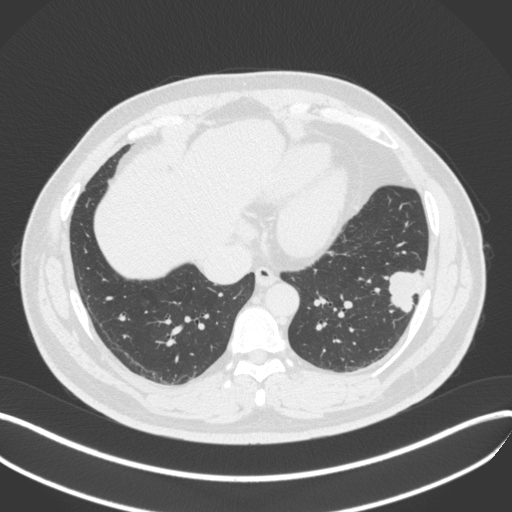
Chest CT, one axial slice. Slice 133 of 420 in the series (ordered by position). 120 kVp. Lung window (W 1500 / L -600 HU). 1 mm slice thickness. 512 × 512 image matrix, field of view 400 × 400 mm. Patient: male, 39 years. Case-level facts recorded for this patient, not image findings: clinical TNM (as recorded): T2a N0 M0.
Structures marked on this image (bounding box drawn by a radiologist):
- lung tumour (recorded histology: adenocarcinoma): box from (x=385, y=265) to (x=427, y=318) px